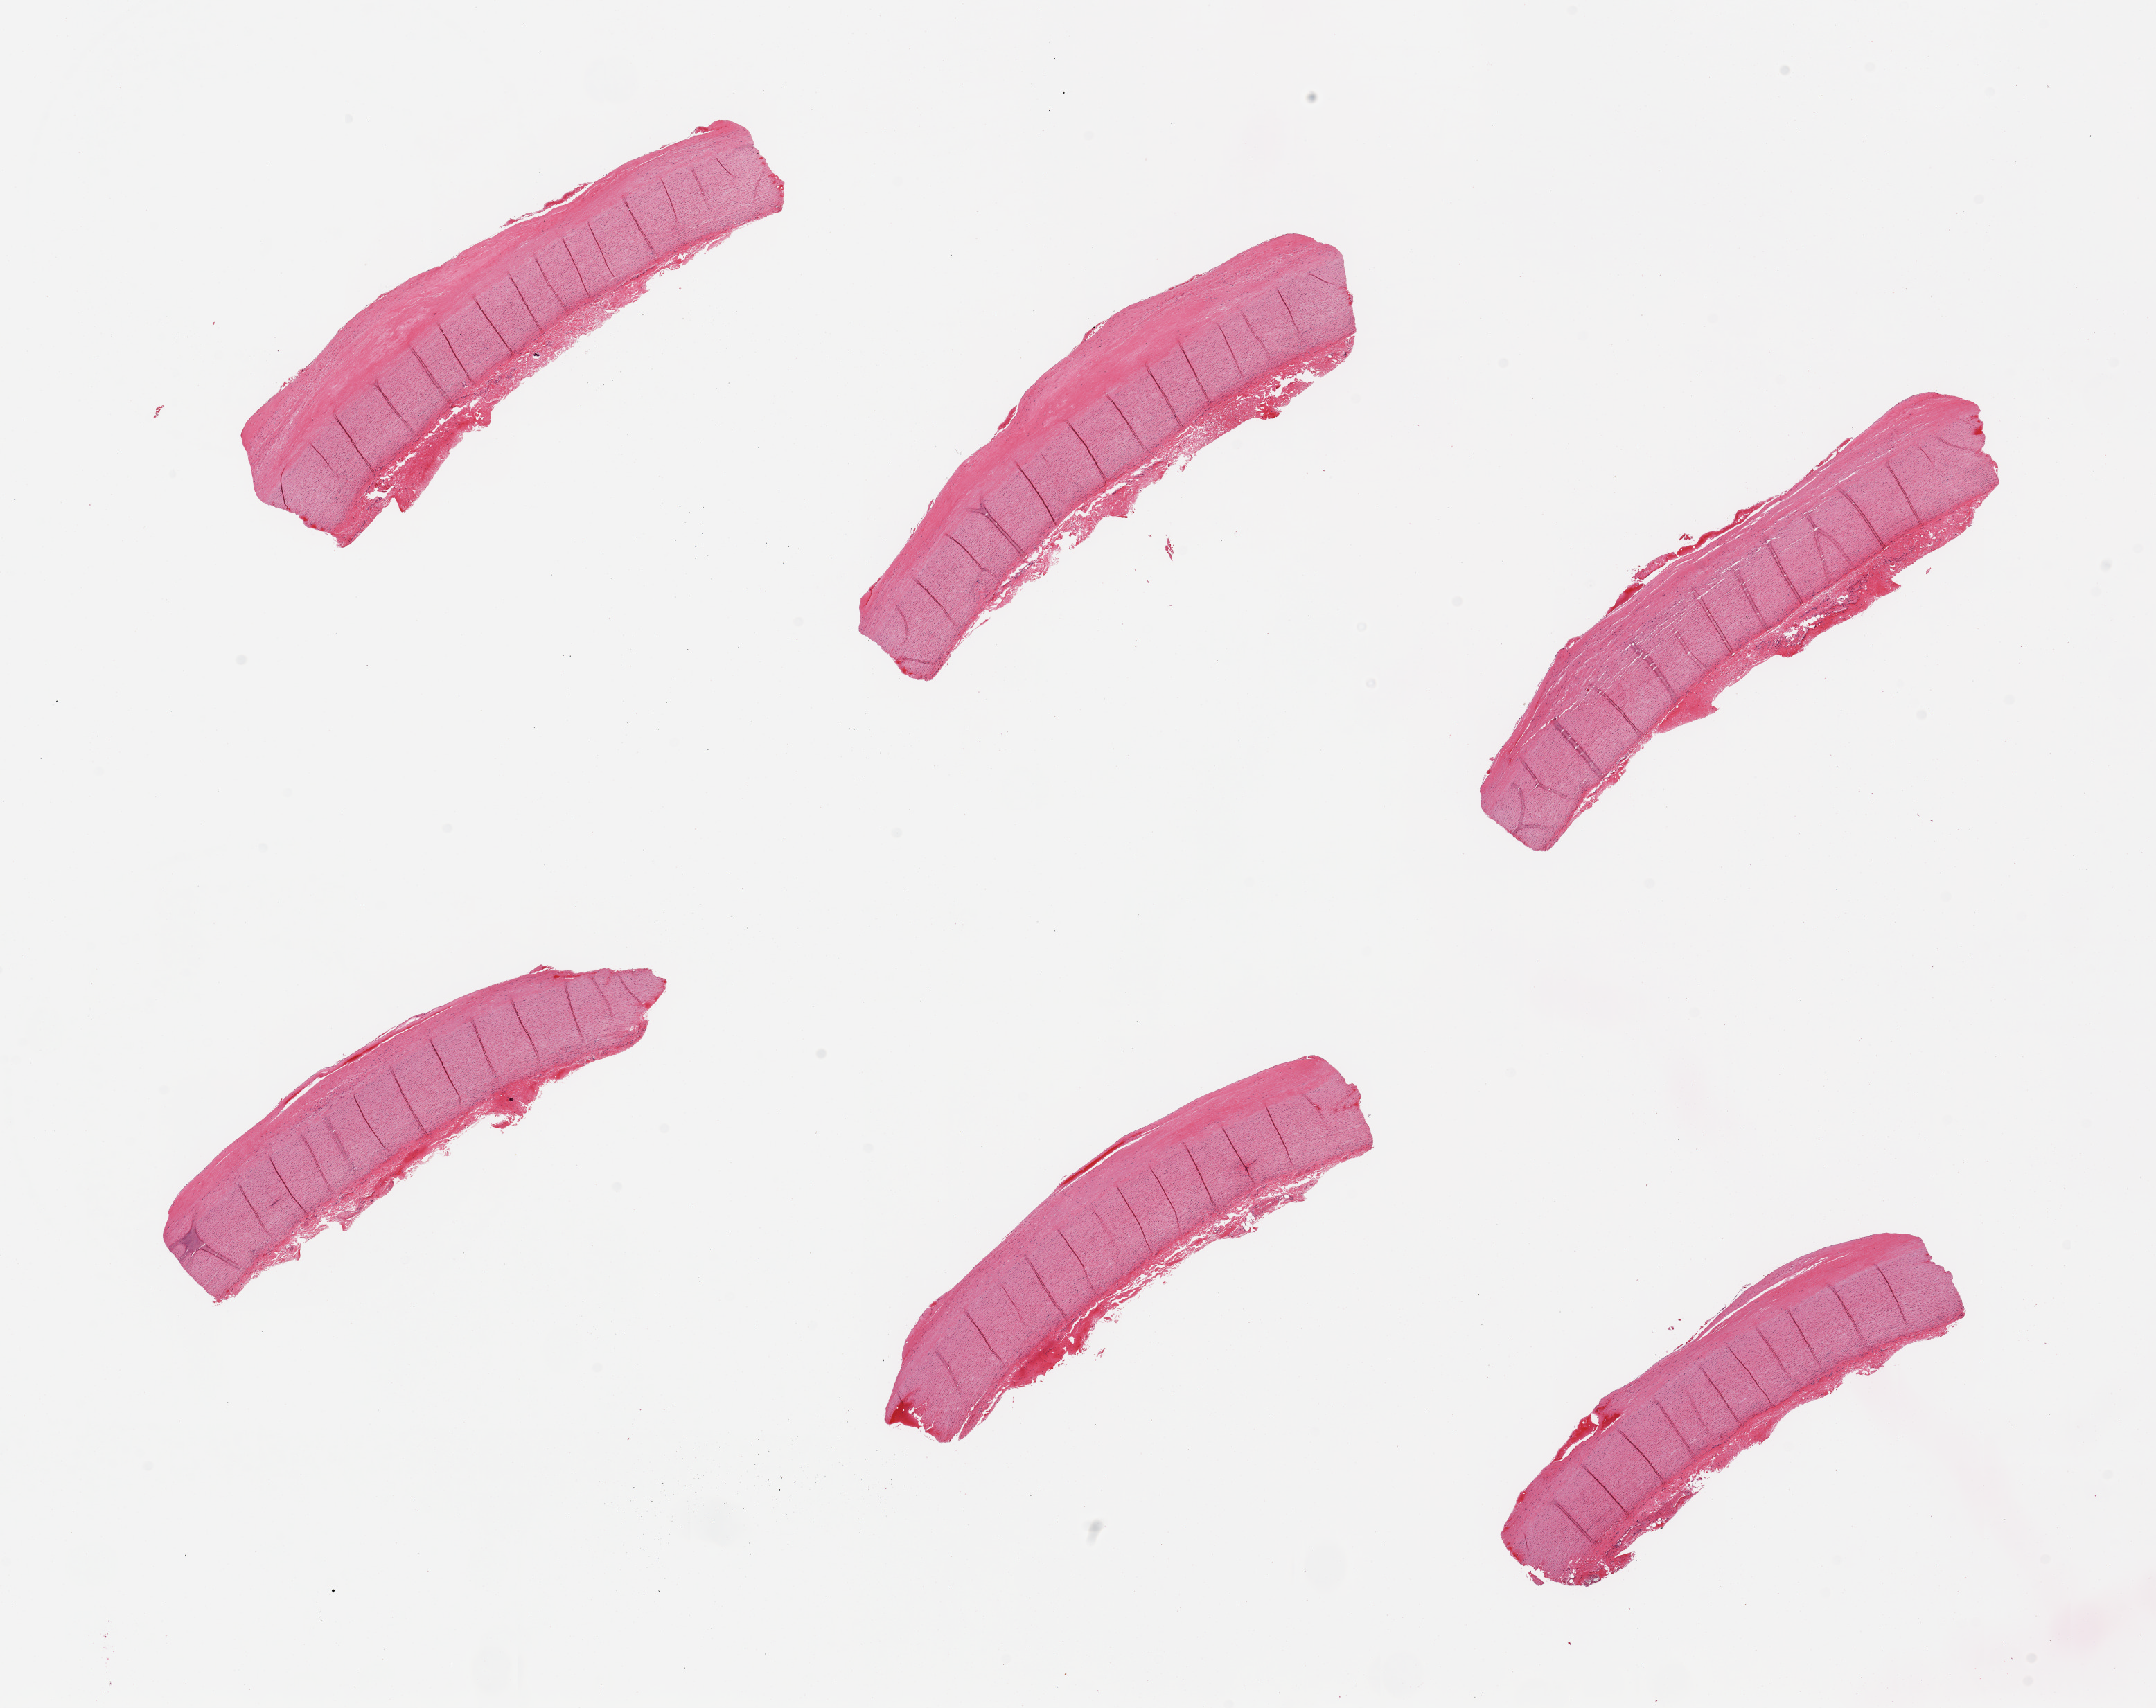
Whole-slide image, hematoxylin and eosin (H&E) stain, whole scanned area (about 24.6 x 19.5 mm, from a 20x scan) shown as a low-resolution overview. PAXgene-fixed paraffin-embedded (PFPE) section. Target tissue: aorta. Tissue donor sample.
- reviewer comment on this tissue sample: 6 pieces, atherosis up to ~0.7mm, ~40% thickness